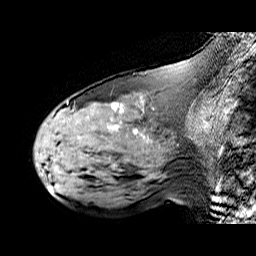
Breast MRI (dynamic contrast-enhanced), one sagittal slice. Position 26 of 60 along the scan axis. Dynamic contrast-enhanced series, time point 2 of 6 at this slice position (early post-contrast). 1.5 T. TE 6.3 ms, TR 32.9 ms. 256 × 256 image matrix, field of view 200 × 200 mm. Female patient. From the clinical record (not read from this slice): setting: breast cancer imaged before/during neoadjuvant chemotherapy; receptor status: HER2-positive.
Structures marked on this image (semi-automatic segmentation, software-assisted and operator-edited):
- analysis volume of interest (the breast-tissue region the enhancement analysis was run in; not a lesion): bounding box <48,92,195,174> (left, top, right, bottom; pixels)
- tumour enhancement mask (voxels above the 100 % enhancement threshold inside the analysis volume of interest): <108,104,122,129>